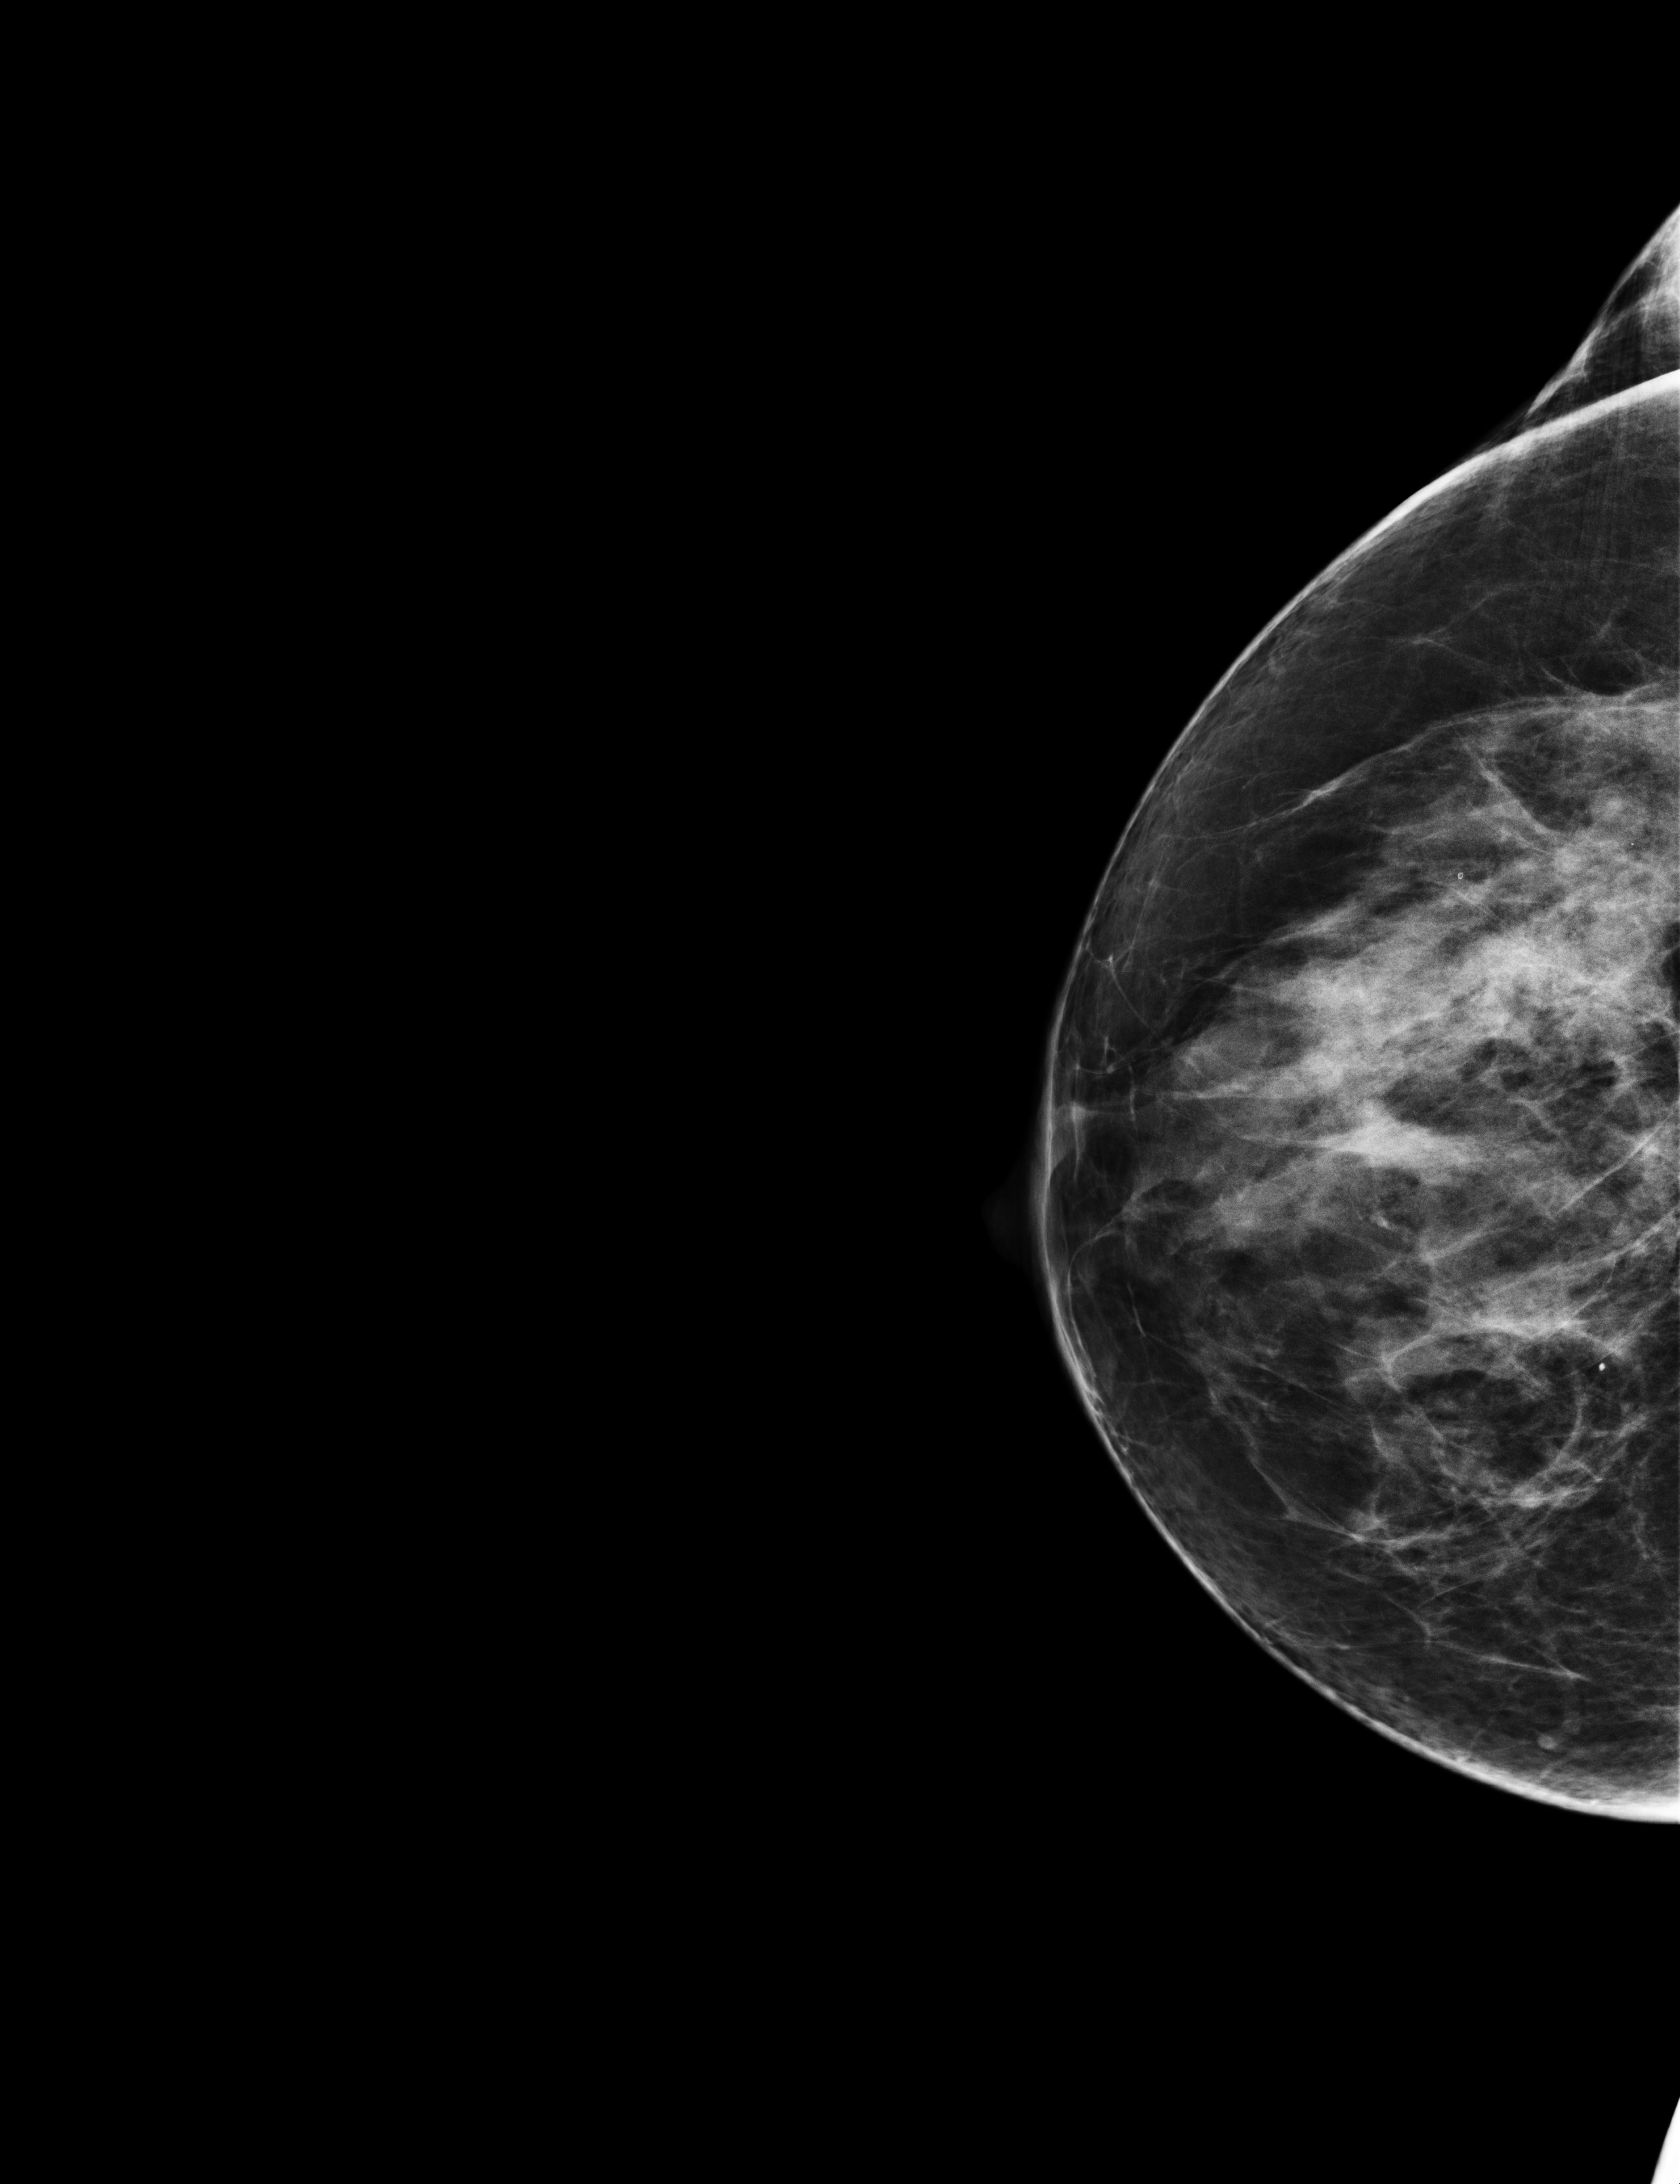
Full-field digital mammogram (FFDM); right breast; CC view; screening examination; compressed breast thickness 64 mm; system: Selenia Dimensions. Female patient, age 59 years.
Final BI-RADS category for the screening round (tomosynthesis exam, both breasts): category 2.